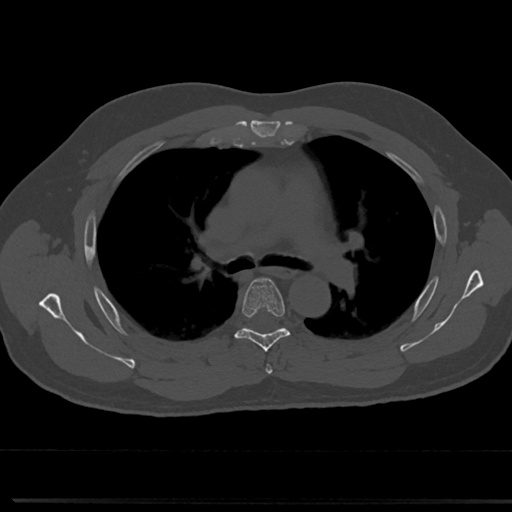
CT including the spine, one axial slice; reconstruction kernel Br40s/3; 120 kVp; bone window (W 1800 / L 400 HU); 512 × 512 image matrix. Patient: male, 61 years. From the clinical record (not read from this slice): primary cancer: prostate.
Annotated regions visible in this slice (semi-automatically segmented with operator editing):
- T4 vertebra: bounding box (x1, y1, x2, y2) in pixels: (264, 355, 273, 374)
- T5 vertebra: (218, 277, 308, 351)